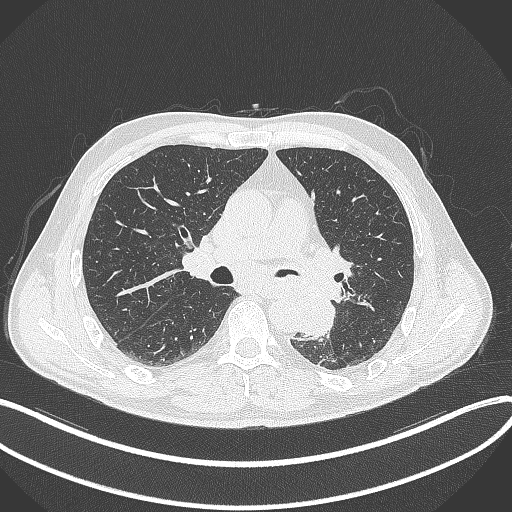
Chest CT, one axial slice; slice 200 of 329 in the series (ordered by position); lung window (W 1500 / L -600 HU); 512 × 512 image matrix, field of view 400 × 400 mm. Male patient, age 59 years. From the clinical record (not read from this slice): clinical TNM (as recorded): T2a N2 M0.
Annotated regions visible in this slice (rectangle marked by the reading radiologist):
- lung tumour (recorded histology: squamous cell carcinoma): box from (x=292, y=287) to (x=336, y=338) px